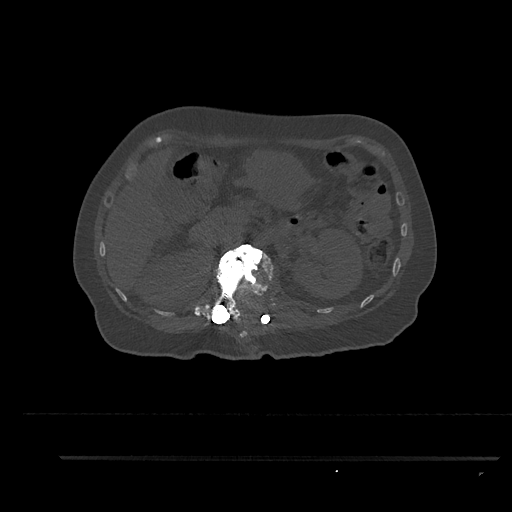
CT including the spine, one axial slice; reconstruction kernel Br40s/3; bone window (W 1800 / L 400 HU); 512 × 512 image matrix. Female patient, age 44 years. From the clinical record (not read from this slice): primary cancer: renal.
Annotated regions visible in this slice (semi-automatically segmented with operator editing):
- L1 vertebra: bounding box <204,243,274,326> (left, top, right, bottom; pixels)
- T12 vertebra: <230,313,248,338>